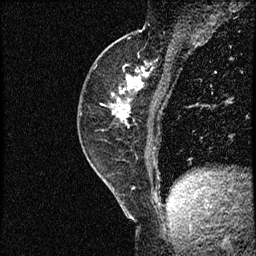
Breast MRI (dynamic contrast-enhanced), one sagittal slice; position 27 of 56 along the scan axis; dynamic contrast-enhanced study with each time point stored as its own series, time point 2 of 3 at this slice position (early post-contrast, ordered by acquisition time); 1.5 T; TE 4.2 ms, TR 17.3 ms; 2 mm slice thickness; 256 × 256 image matrix, field of view 200 × 200 mm. Female patient. Case-level facts recorded for this patient, not image findings: setting: breast cancer imaged before/during neoadjuvant chemotherapy; receptor status: HER2-positive.
Structures marked on this image (semi-automatically segmented with operator editing):
- analysis volume of interest (the breast-tissue region the enhancement analysis was run in; not a lesion): box from (x=78, y=50) to (x=156, y=155) px
- tumour enhancement mask (voxels above the 100 % enhancement threshold inside the analysis volume of interest): (x=101, y=73)–(x=148, y=120)